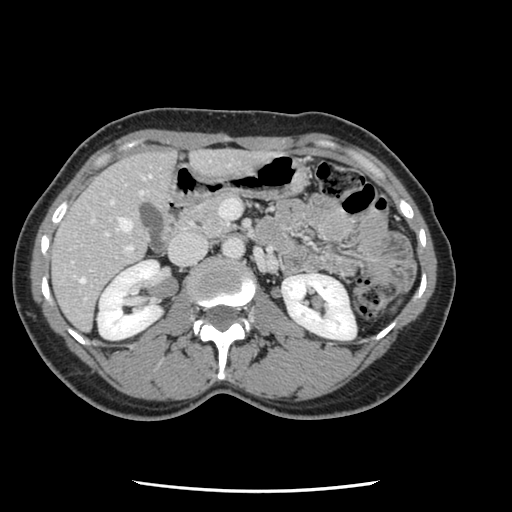
Contrast-enhanced abdominal CT, one axial slice; slice 49 of 134 in the series (ordered by position); 120 kVp; intravenous contrast given; soft-tissue window (W 400 / L 40 HU); 2.5 mm slice thickness; 512 × 512 image matrix, field of view 330 × 330 mm. Female patient, age 43 years. From the clinical record (not read from this slice): diagnosis: colorectal cancer liver metastases, imaged before liver resection; multiple liver metastases: yes; largest metastasis: 3.4 cm.
Annotated regions visible in this slice (outlined manually by an expert reader):
- hepatic veins: bounding box <79,175,151,284> (left, top, right, bottom; pixels)
- liver: <52,151,261,329>
- planned liver remnant (the part of the liver to remain after resection): <52,152,175,329>
- portal vein (with intrahepatic branches): <71,201,241,301>